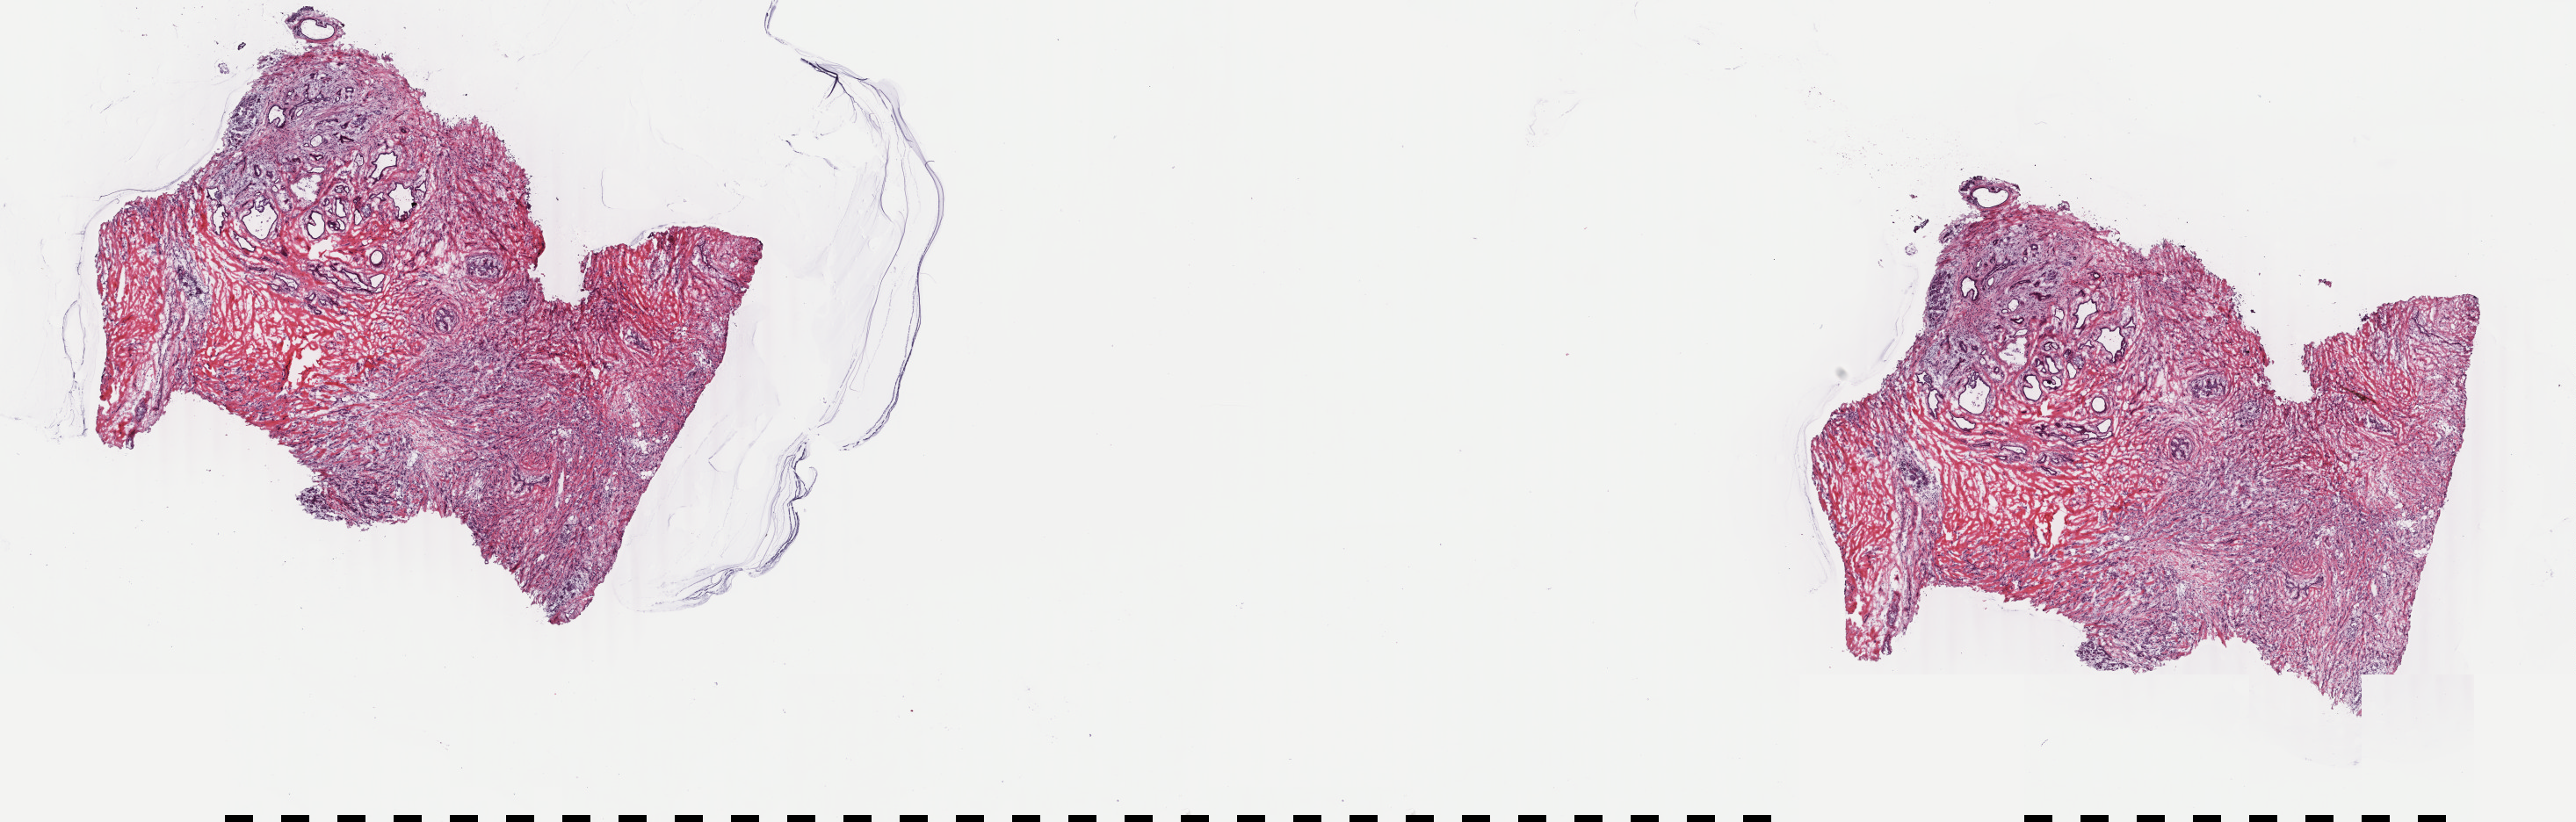
Whole-slide histology image, H&E, a low-resolution overview of the entire scanned area, about 23.3 x 7.4 mm; frozen section from the top of the tissue portion; primary tumour sample from the breast. Female patient; age at initial diagnosis 48 years. Slide review estimates, as recorded: tumour cells 70%, tumour nuclei 70%, normal cells 0%, stromal cells 30%, necrosis 0%. Infiltration values recorded for this section: lymphocyte infiltration 40%, monocyte infiltration 20%, neutrophil infiltration 20%.
Lymph nodes positive (case pathology): 21 of 24 examined. Pathologic diagnosis: Lobular carcinoma, NOS. AJCC pathologic stage: IIIC.